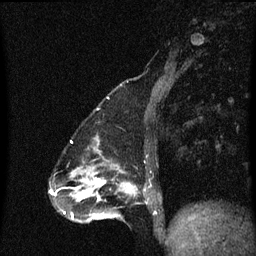
Breast MRI (dynamic contrast-enhanced), one sagittal slice; position 21 of 60 along the scan axis; dynamic contrast-enhanced series, image 2 of 3 at this slice position (ordered by acquisition); 1.5 T; TE 4.2 ms, TR 8.4 ms; 256 × 256 image matrix, field of view 200 × 200 mm. Female patient, age 47 years.
Outlined on this slice (semi-automatically segmented with operator editing):
- analysis volume of interest (the breast-tissue region the enhancement analysis was run in; not a lesion): bounding box <100,172,148,219> (left, top, right, bottom; pixels)
- tumour enhancement mask (voxels above the 70 % enhancement threshold inside the analysis volume of interest): <100,180,136,193>